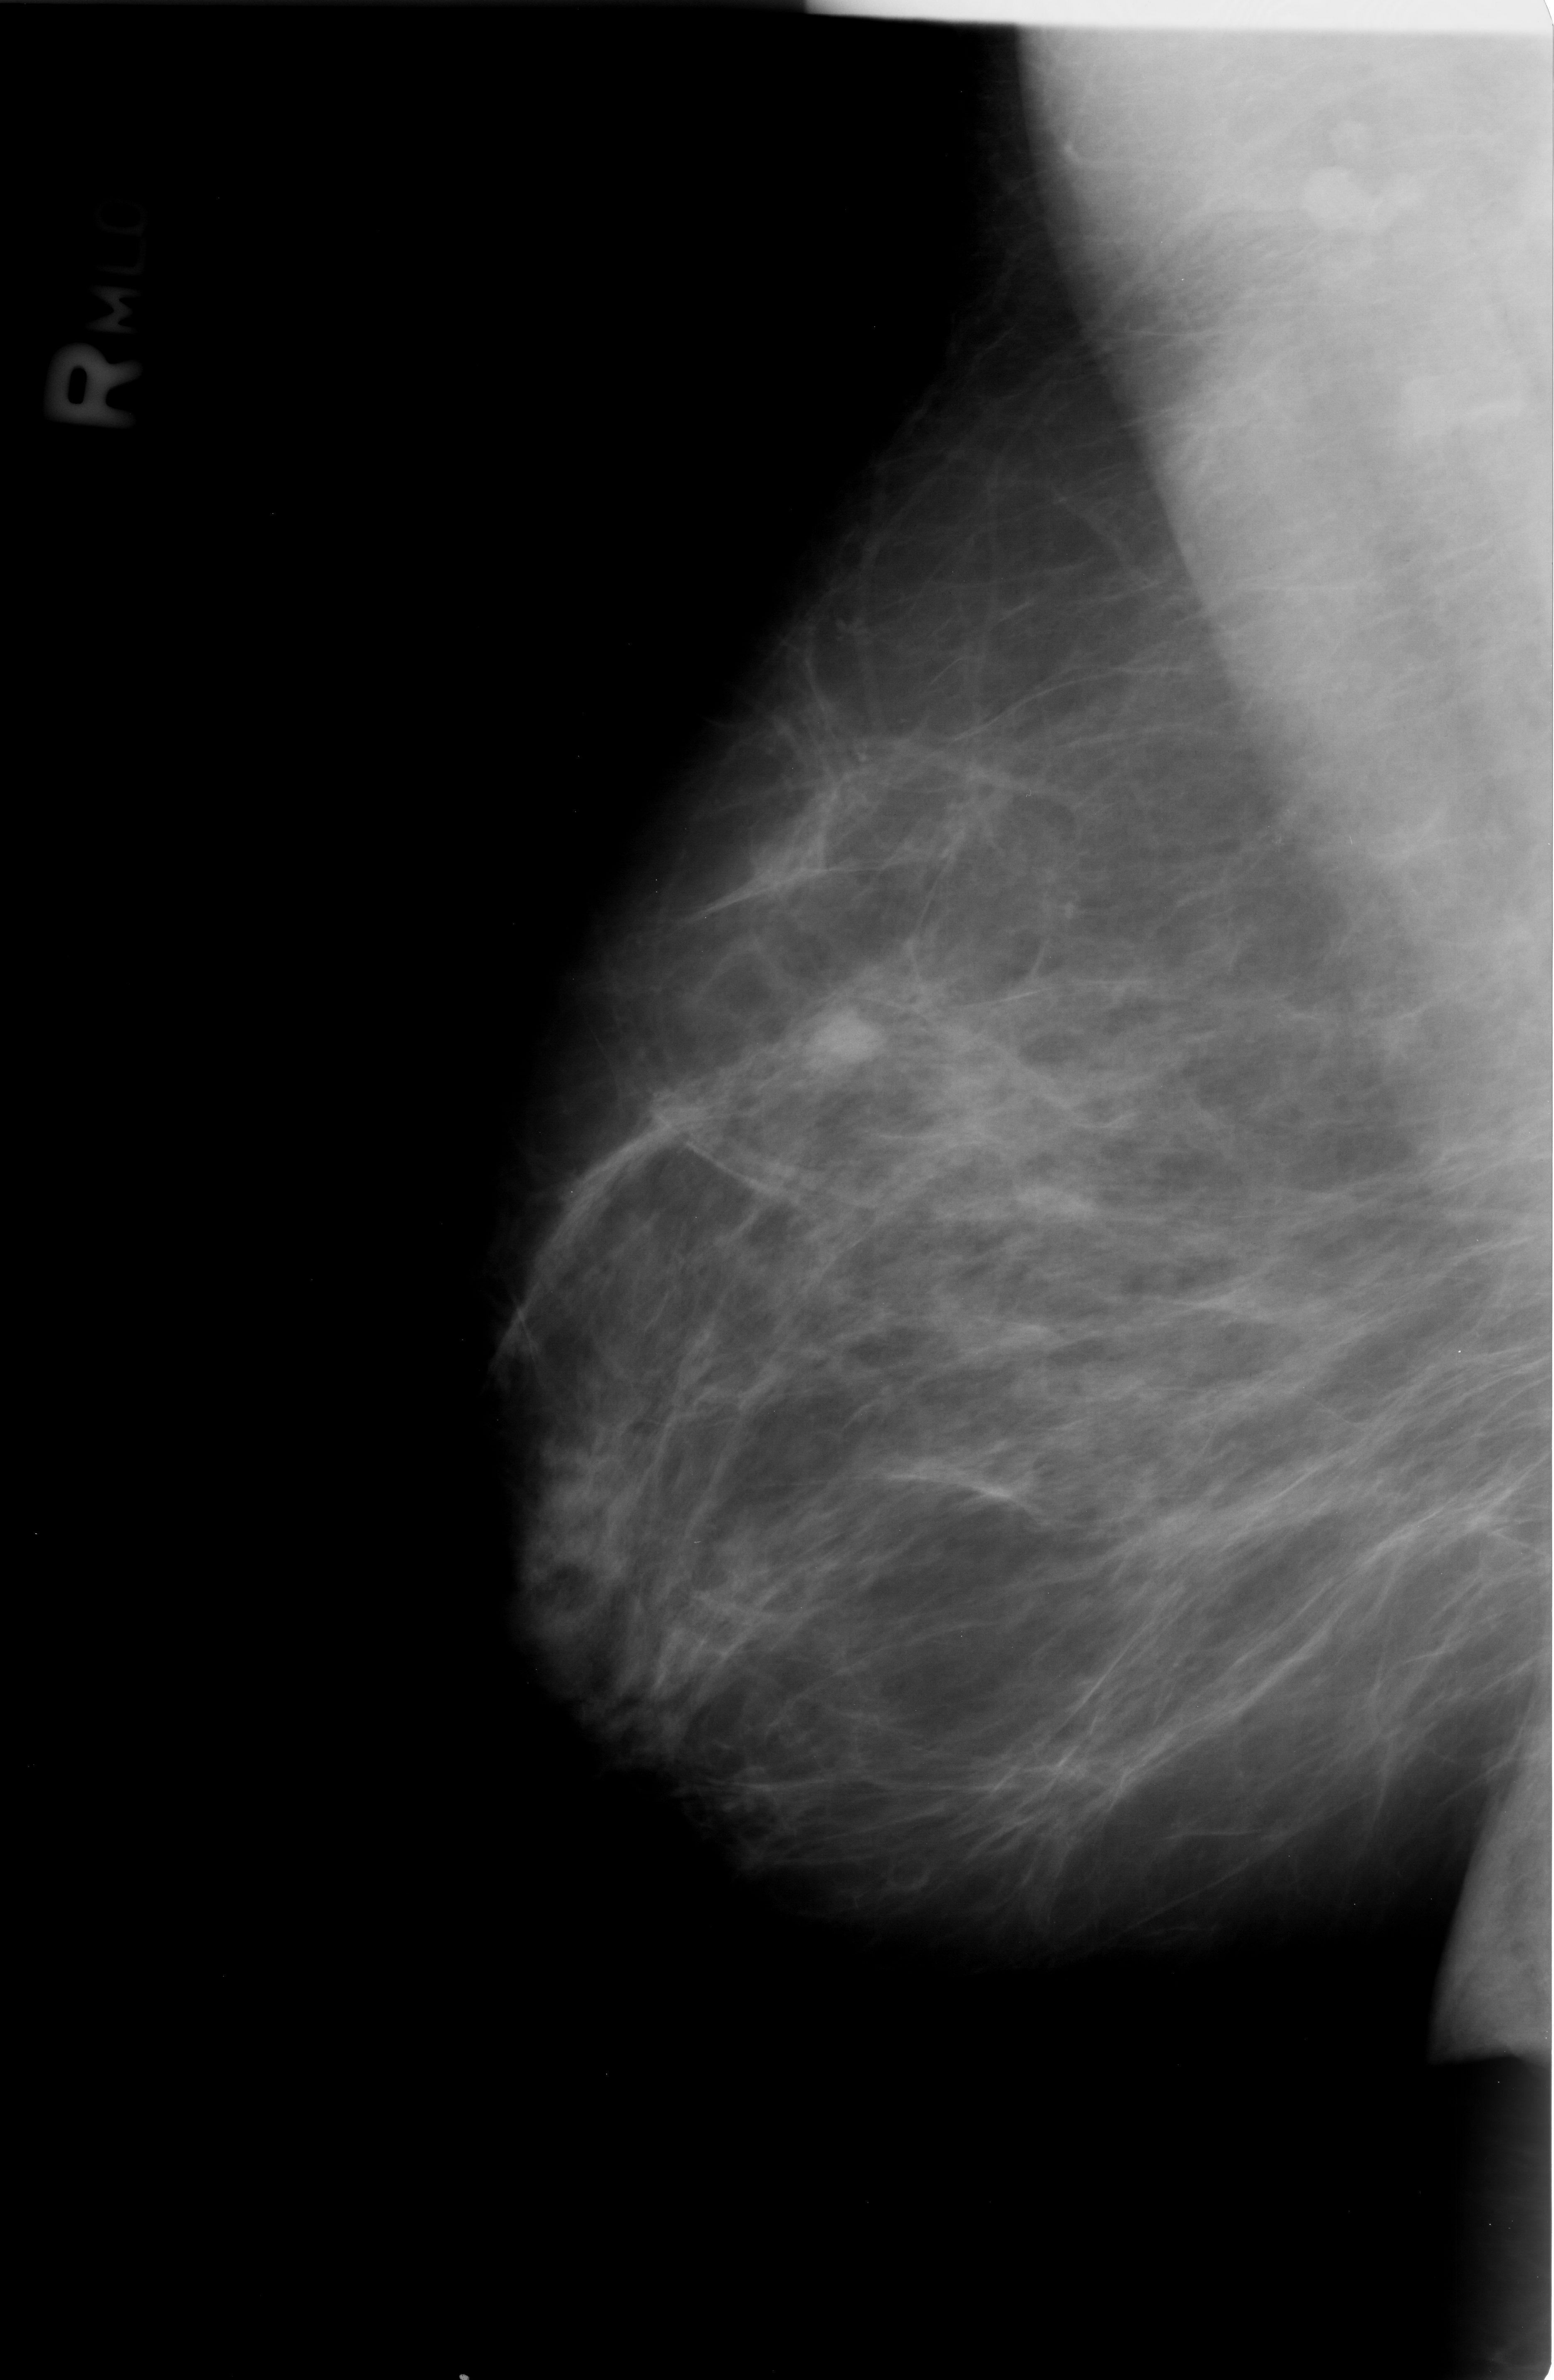
Mammogram (digitized film); right breast; MLO view; BI-RADS breast density category 2 (scale 1–4).
Marked findings (only marked abnormalities are described; nothing is implied about the rest of the image): mass, shape lobulated, margins circumscribed / obscured; BI-RADS assessment category 4; pathology (as recorded): benign.